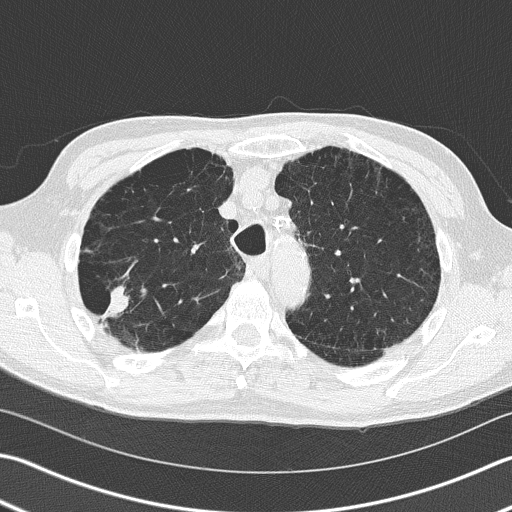
Chest CT (low-dose screening protocol), one axial image. Baseline screening round. Lung window (W 1500 / L -600 HU). Lung (sharp) reconstruction kernel (B50f). Male participant, aged 66 years at enrolment. Current smoker at enrolment.
• Lesion marked by an expert reader, box from (x=80, y=263) to (x=143, y=339) px.
• The exam's reader record, not a measurement of the box and not confirmed to be the same lesion: non-calcified nodule or mass ≥4 mm, right upper lobe, 39 × 23 mm, spiculated (stellate) margins, soft tissue attenuation.